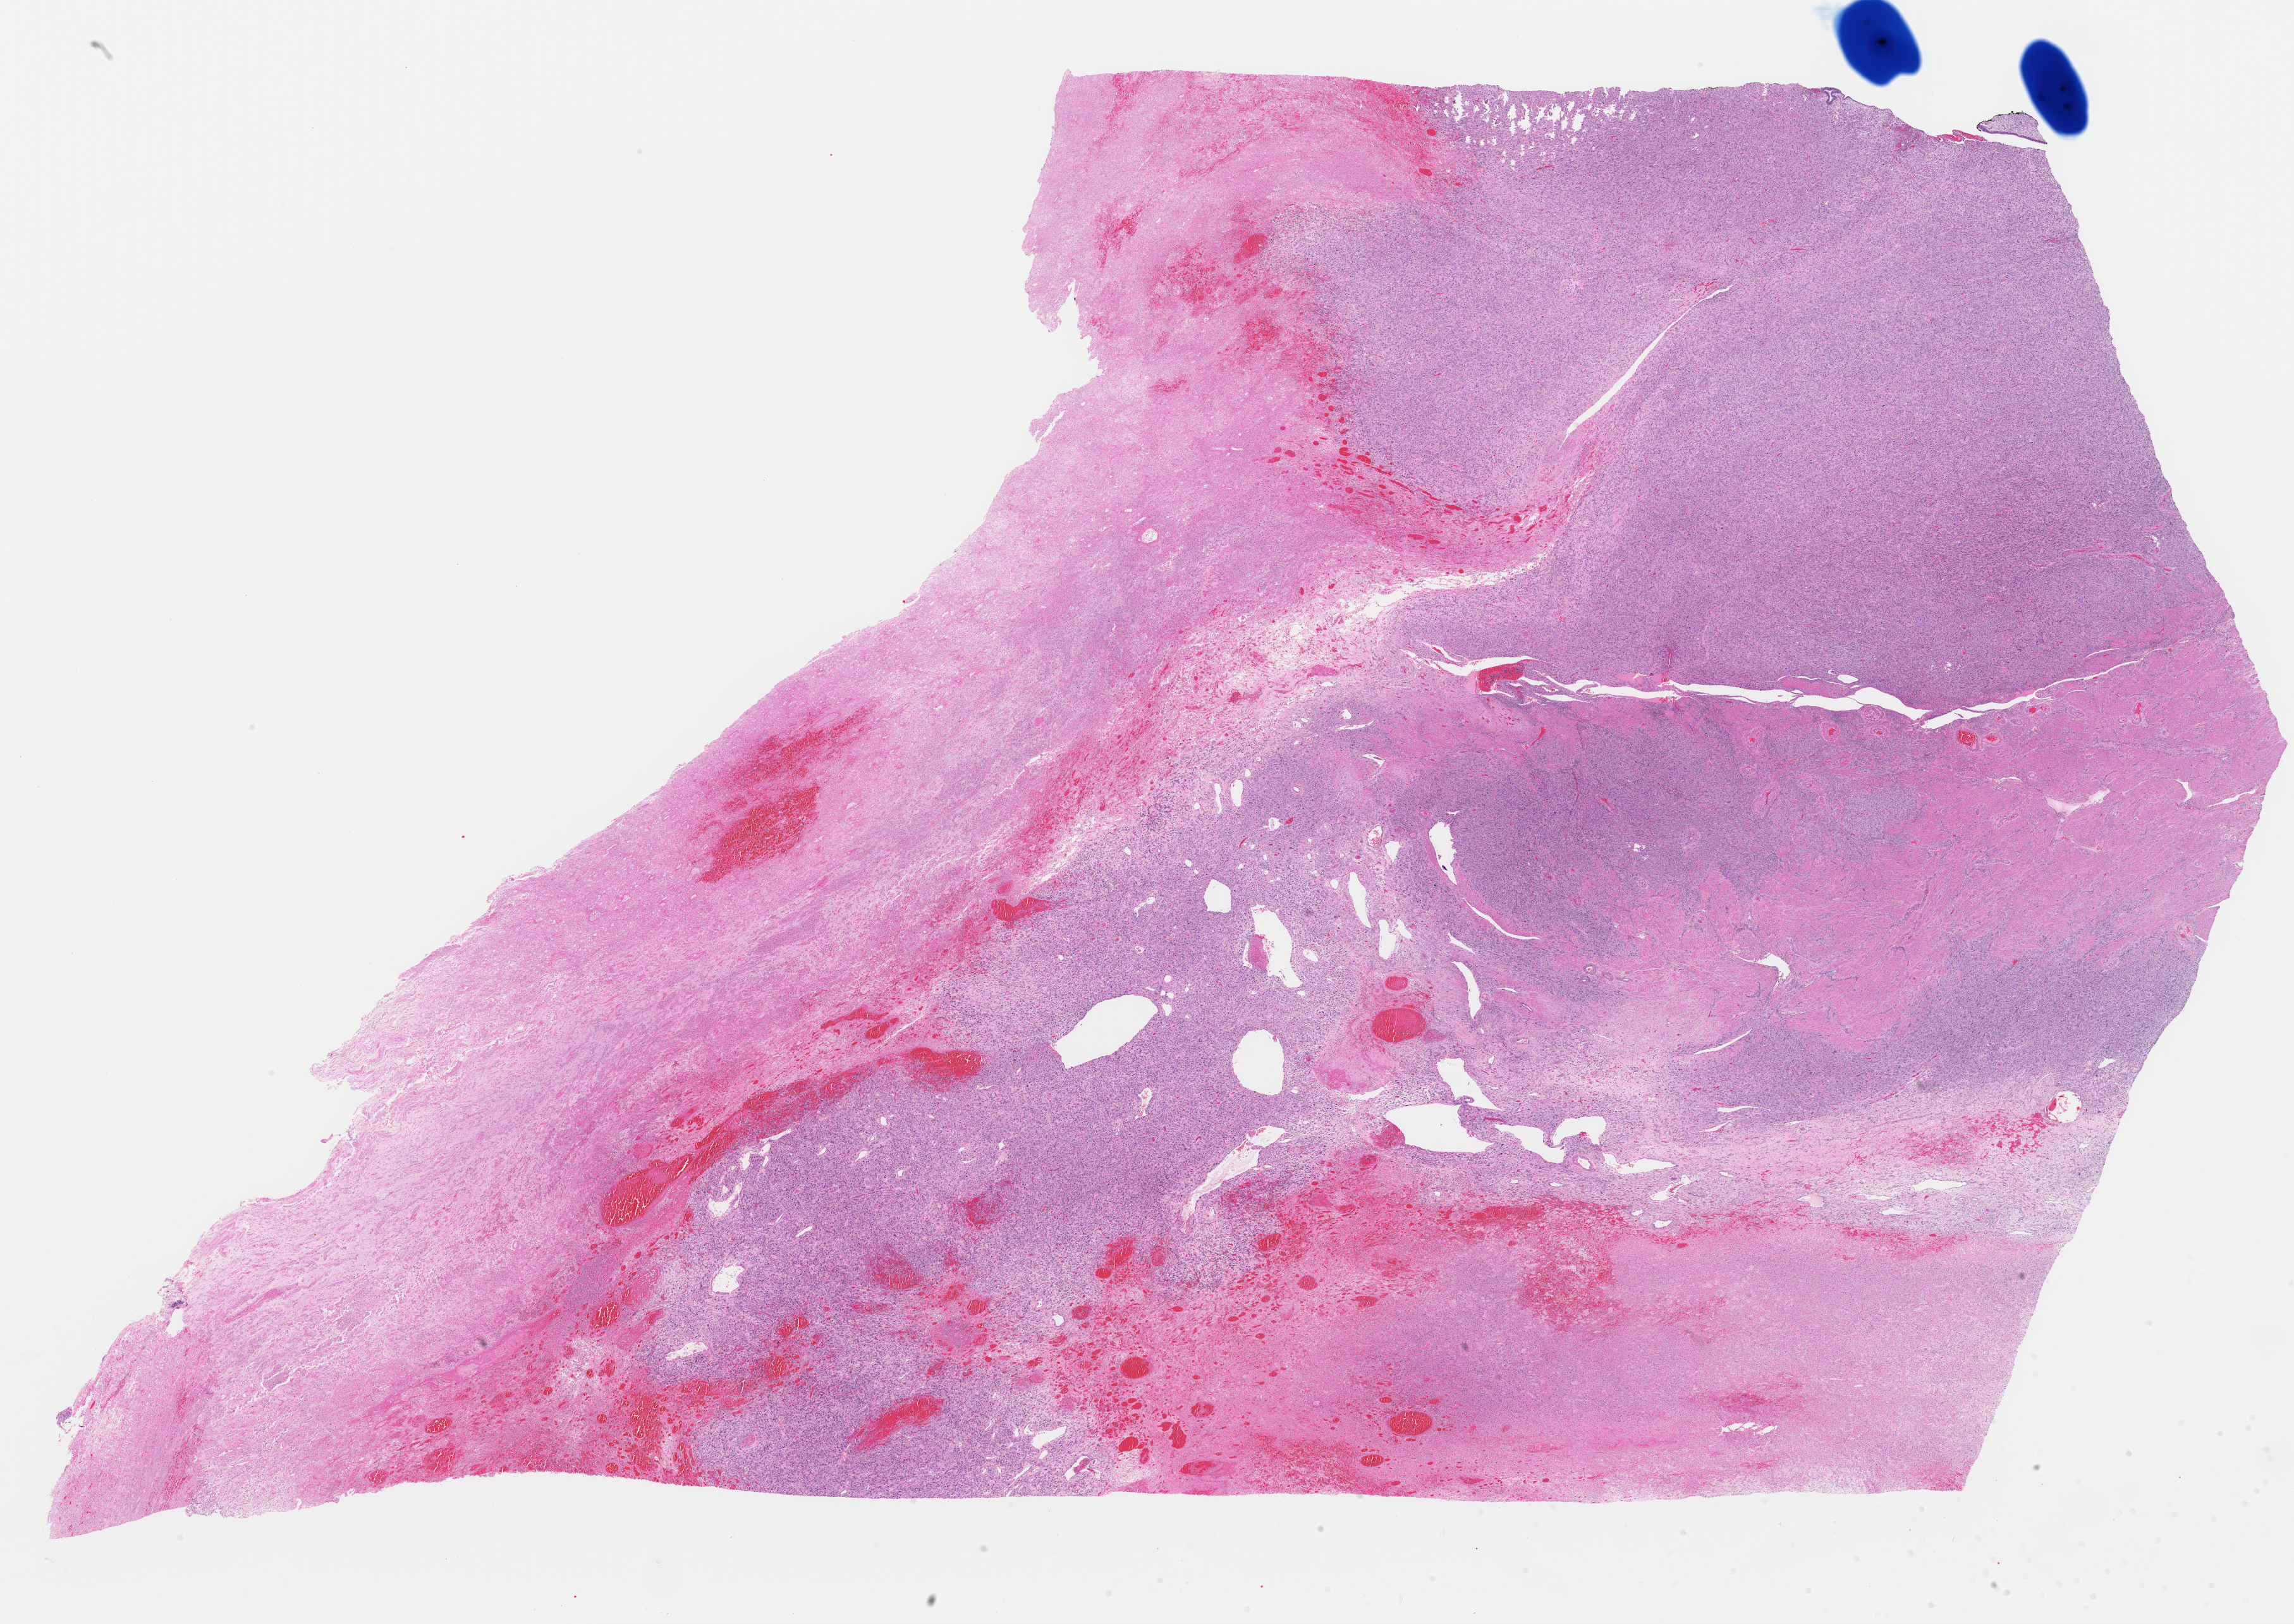
H&E whole-slide image, shown as a low-resolution overview of the whole scanned area (about 28.7 x 20.3 mm). Formalin-fixed paraffin-embedded (FFPE) diagnostic section. Uterus, primary tumour sample. Female patient; age at initial diagnosis 41 years.
Histologic diagnosis: Leiomyosarcoma, NOS.